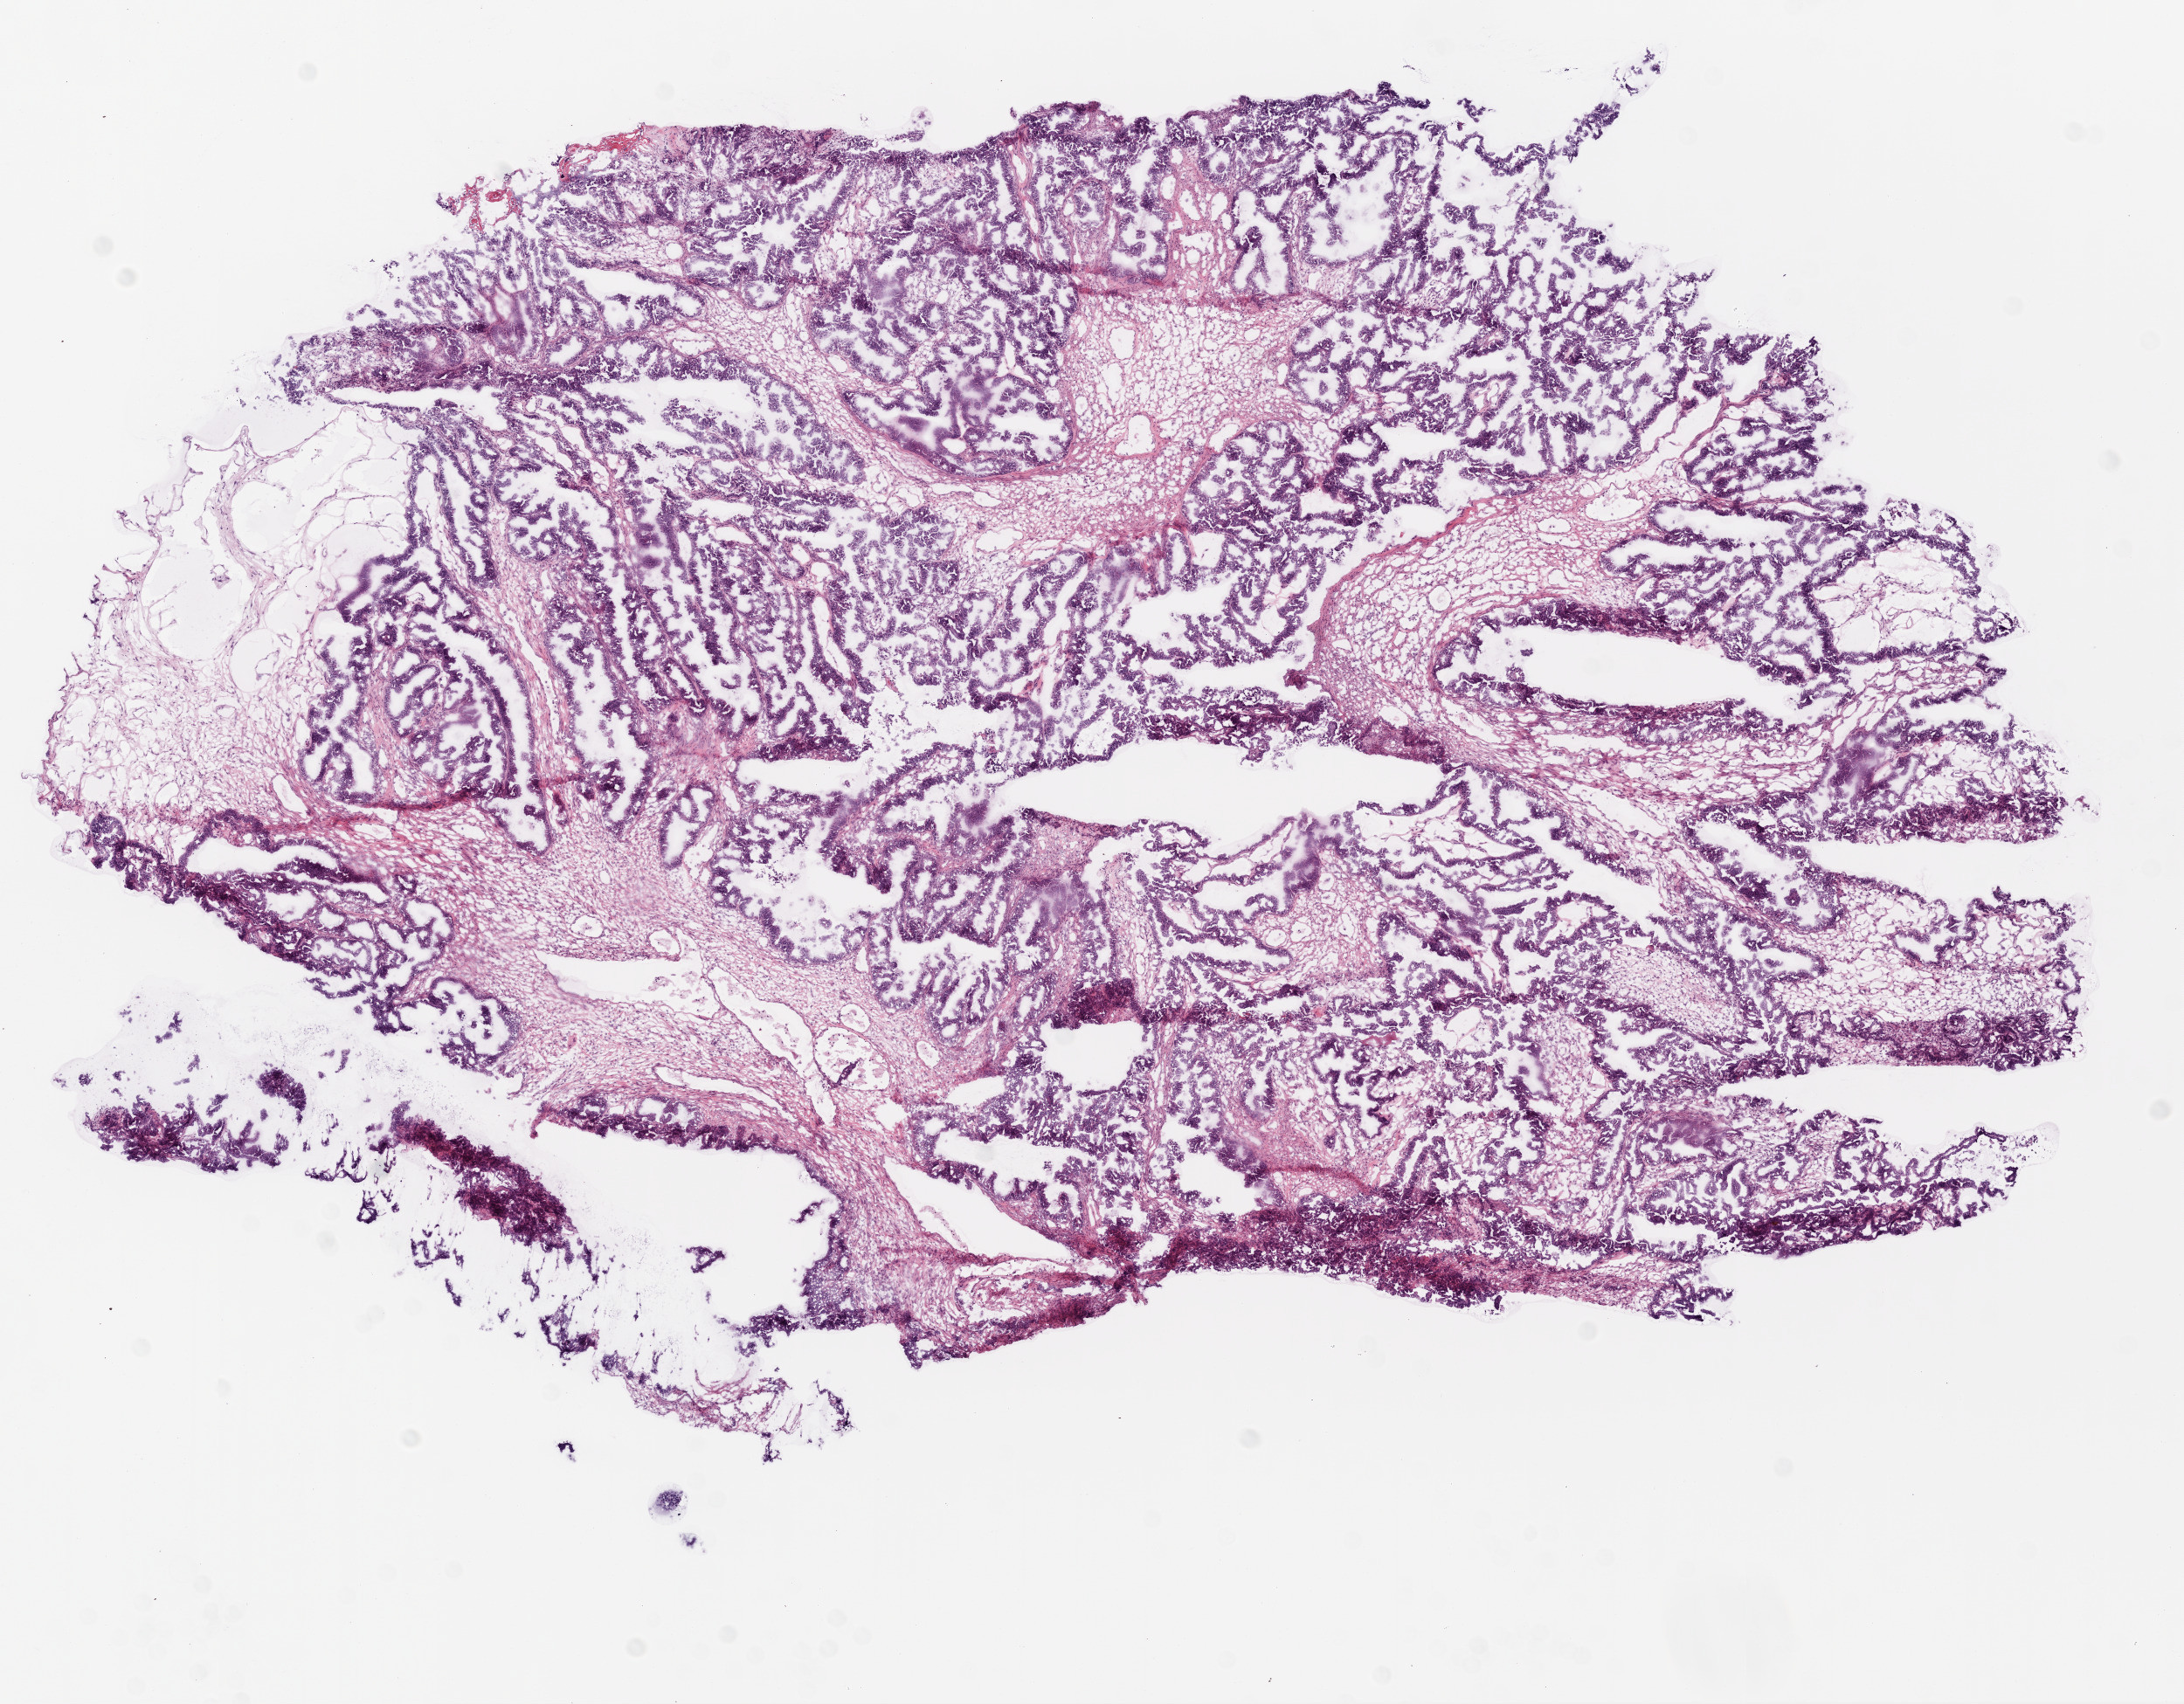
Digitized H&E-stained tissue section (whole slide) — shown as a low-resolution overview of the whole scanned area (about 10.0 x 7.8 mm, from a 20x scan); frozen section from the top of the tissue portion; ovary, primary tumour sample. Patient: female, age at initial diagnosis 58 years.
Pathologic diagnosis: Serous cystadenocarcinoma, NOS.